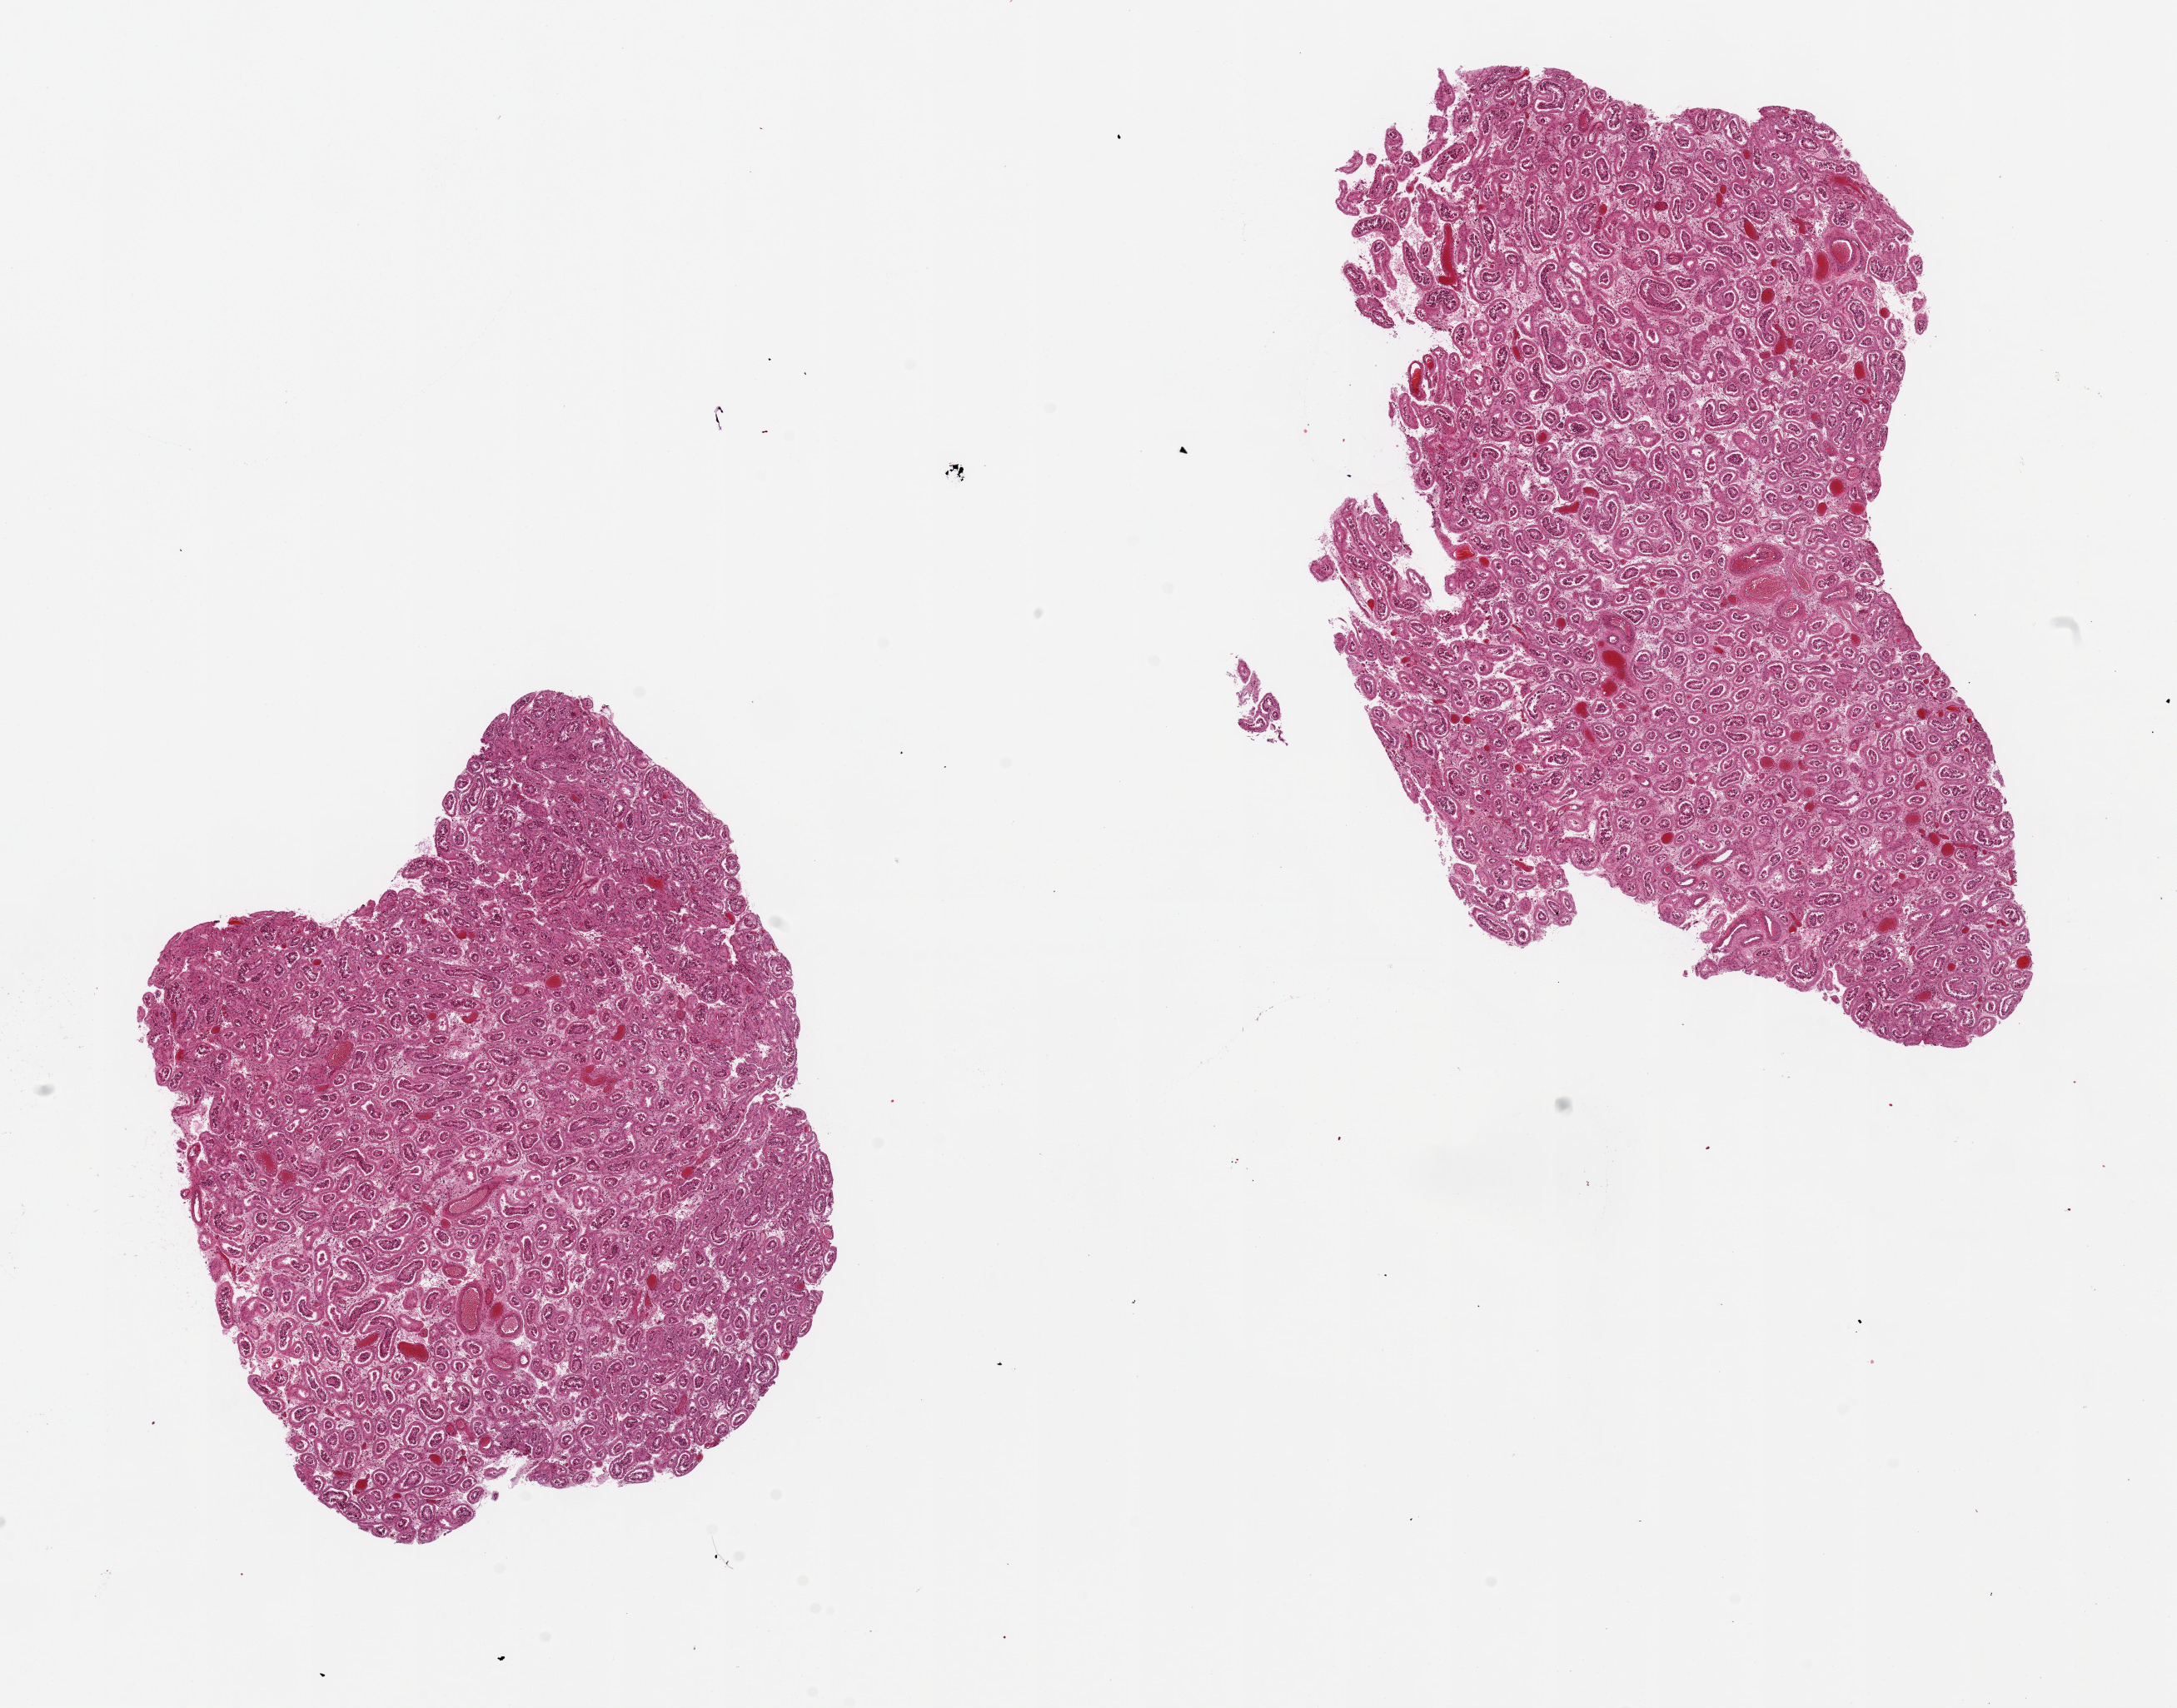
Digitized haematoxylin and eosin-stained section, brightfield, shown as a low-resolution overview of the whole scanned area (about 20.7 x 16.2 mm, acquisition: 20x scan), PAXgene-fixed paraffin-embedded (PFPE) section, target tissue: testis, donor tissue sample. Donor: male.
* reviewer comment on this tissue sample: 2 pieces, 7.5x6 & 10.5x8mm; spermatogenesis severely decreased